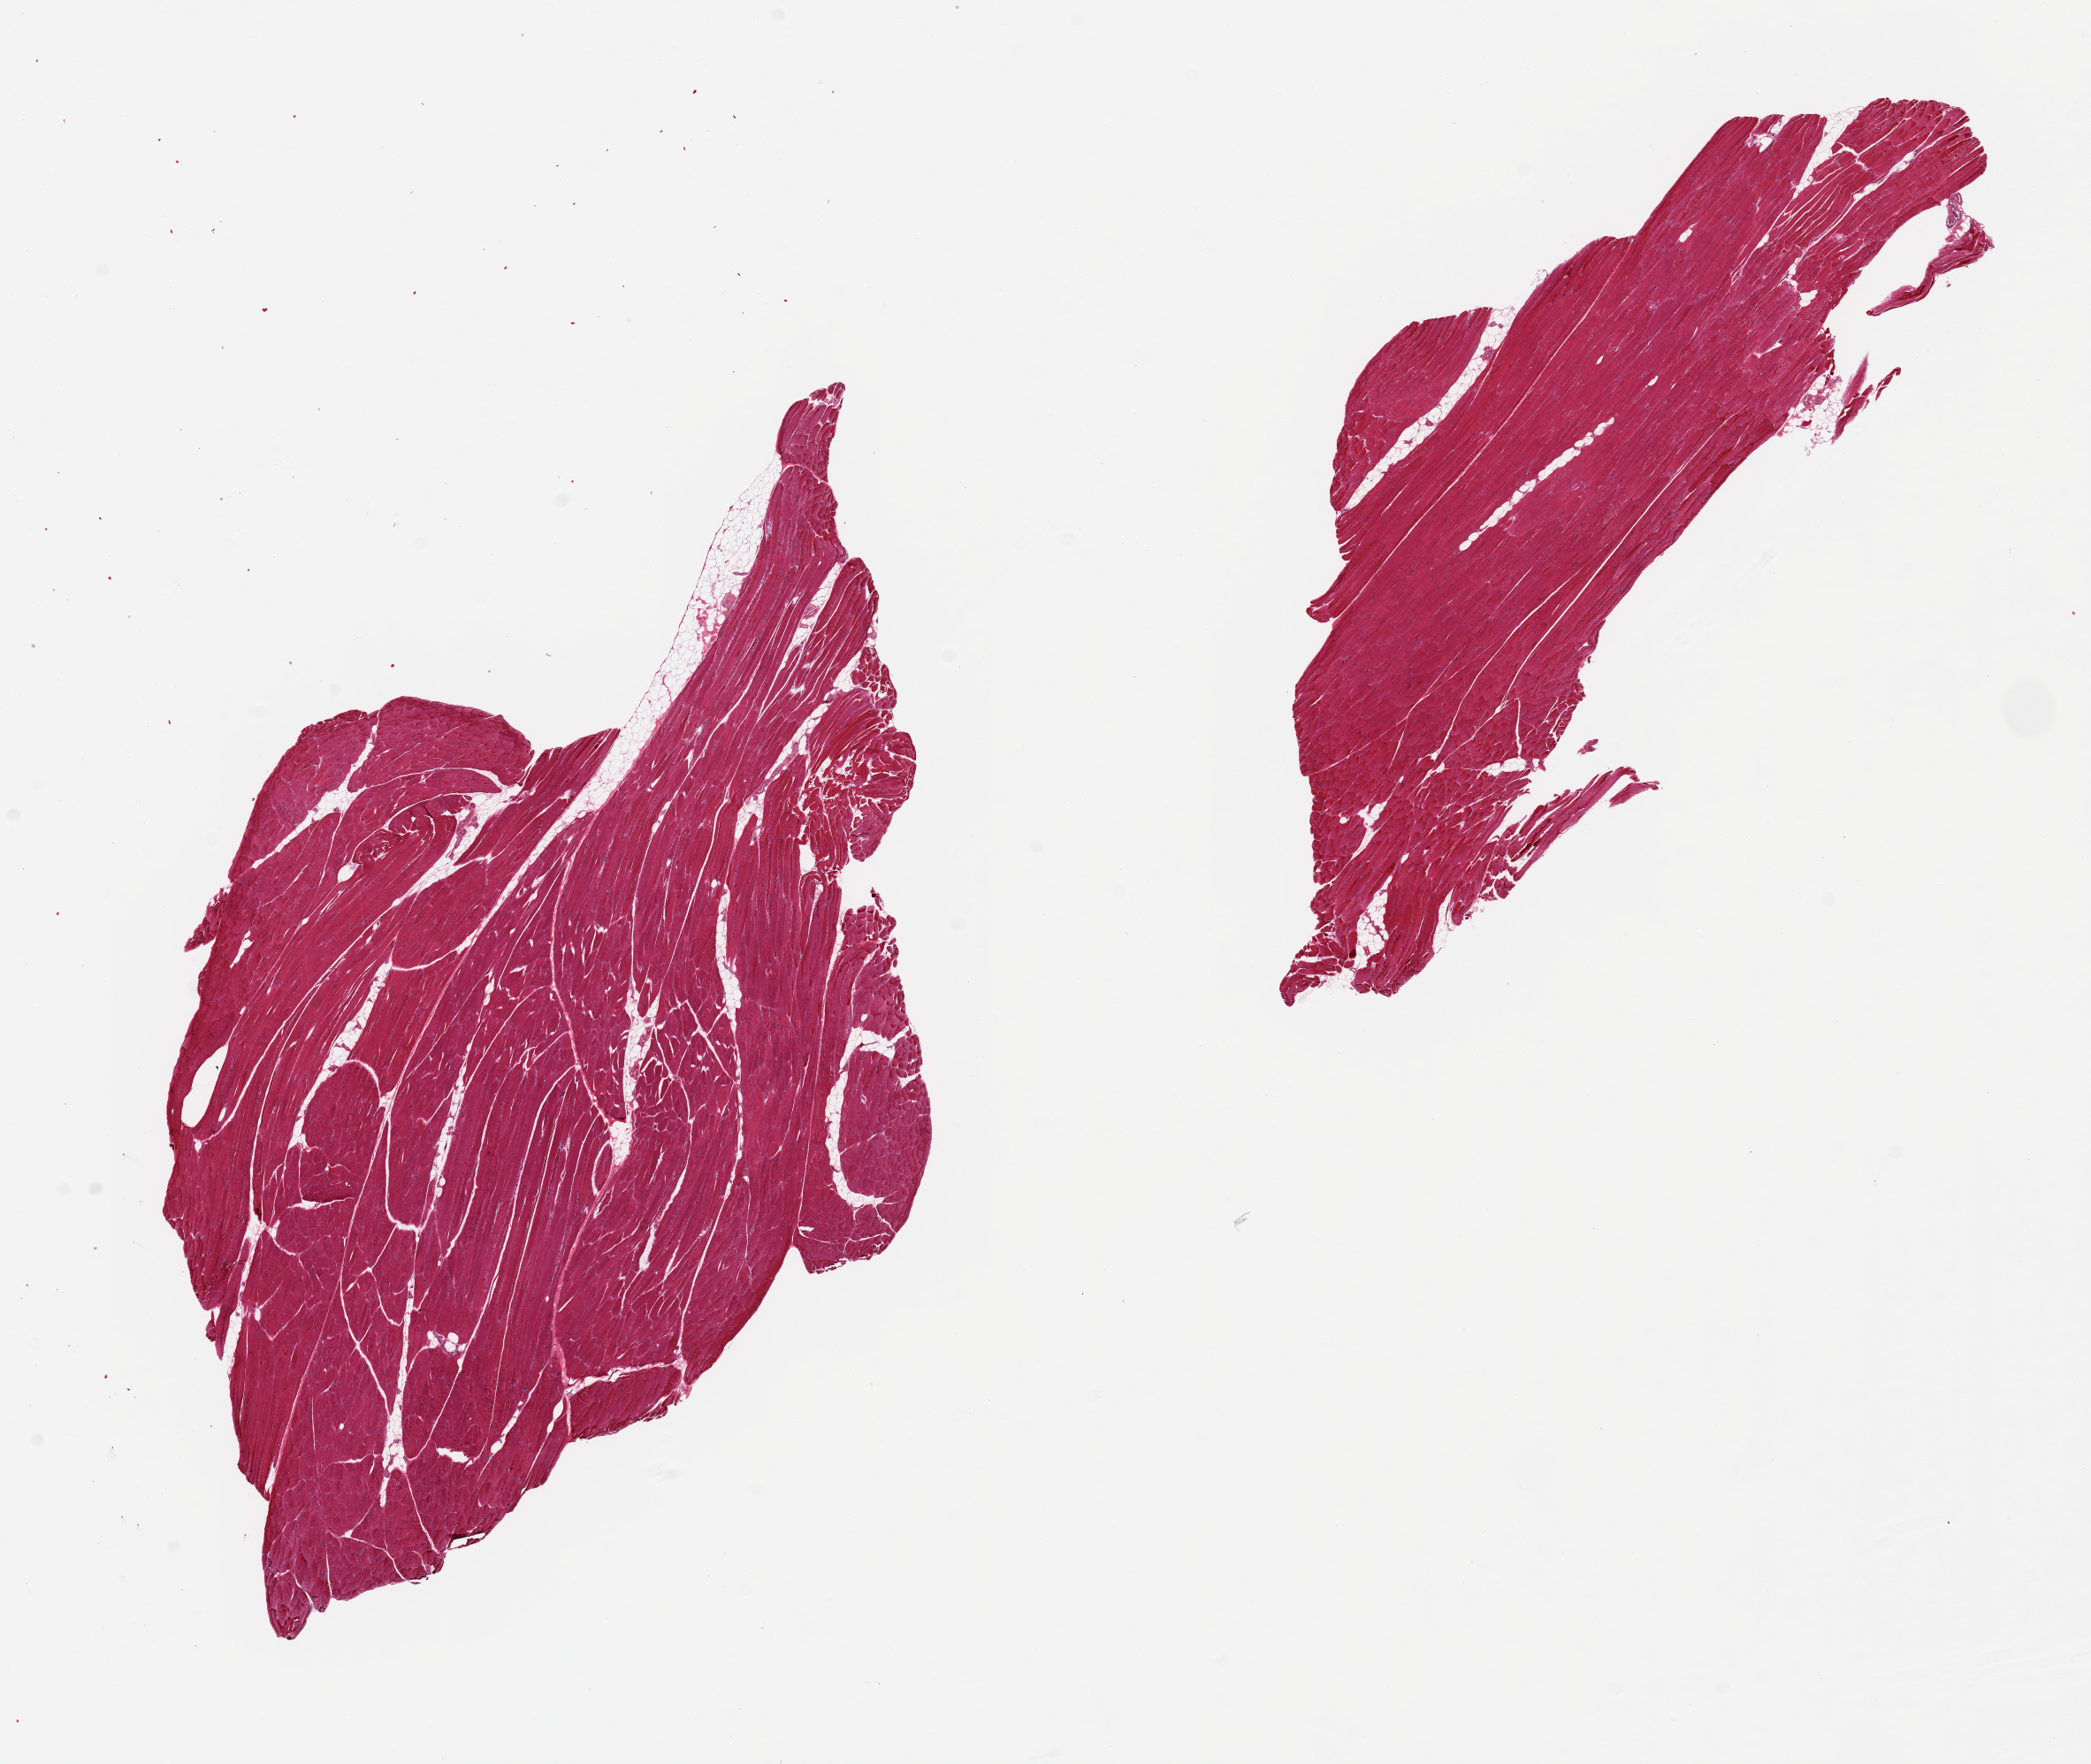
Digitized H&E-stained section, brightfield — a low-resolution overview of the entire scanned area, about 18.7 x 15.8 mm (from a 20x scan); PAXgene-fixed, paraffin-embedded tissue; target tissue: skeletal muscle; donor tissue sample.
- pathologist's review note for this sample: 2 pieces, 8x8 & 10x4mm; minimal adipose